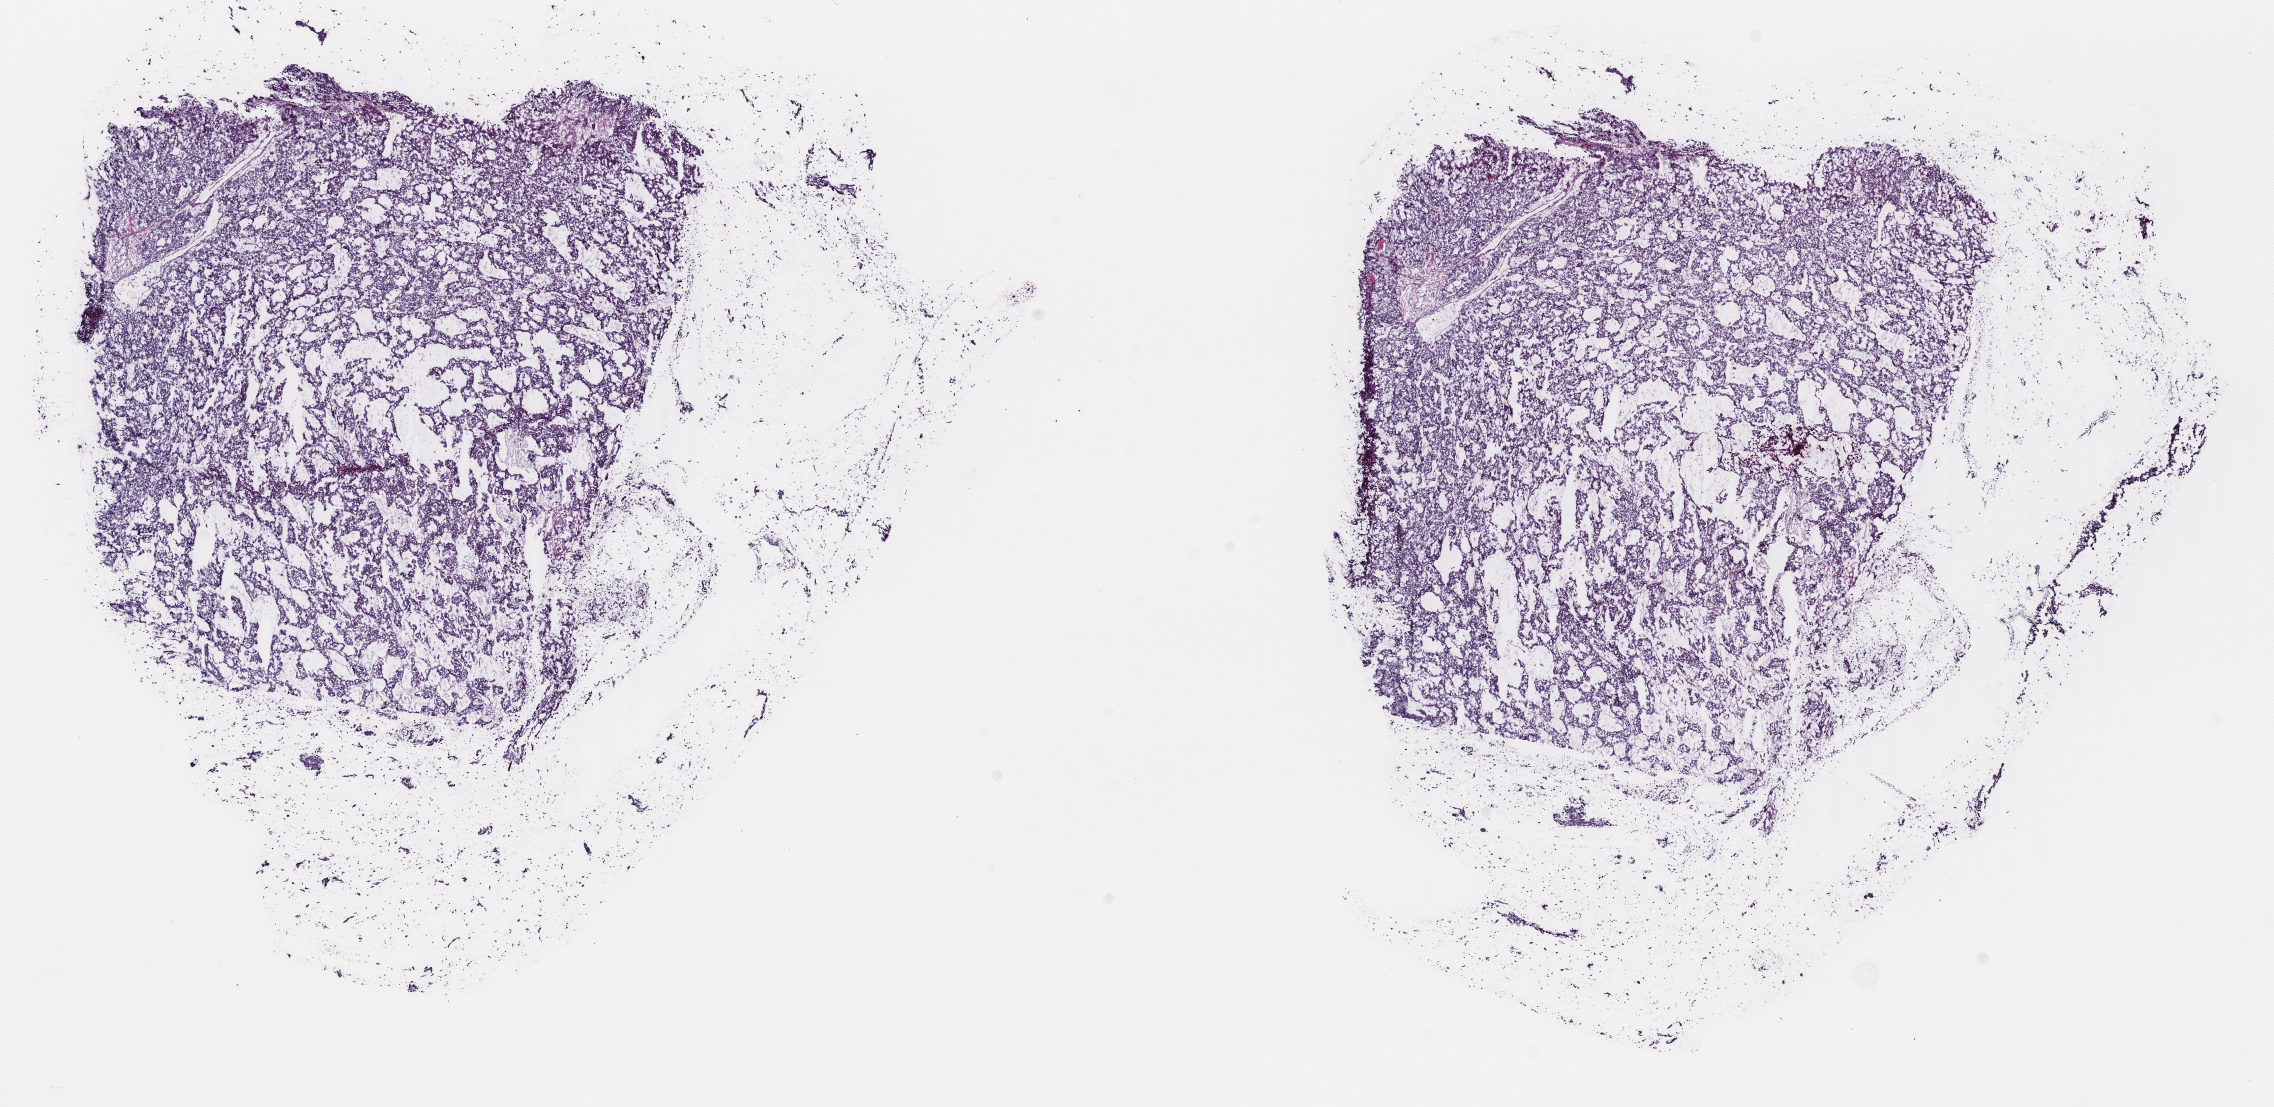
Digitized H&E-stained tissue section (whole slide), whole scanned area (about 18.1 x 8.8 mm, from a 40x scan) shown as a low-resolution overview. Frozen section from the bottom of the tissue portion. Sample: primary tumour, liver. Male patient; age at initial diagnosis 69 years. Histologic grade: G3 (poorly differentiated). Slide review estimates, as recorded: tumour cells 80%, tumour nuclei 80%, normal cells 0%, stromal cells 20%, necrosis 0%. Inflammatory infiltration, as recorded: lymphocyte infiltration 2%, monocyte infiltration 2%, neutrophil infiltration 0%.
Diagnosis: Hepatocellular carcinoma, NOS. AJCC pathologic stage: I. TNM: T1 N0 M0.